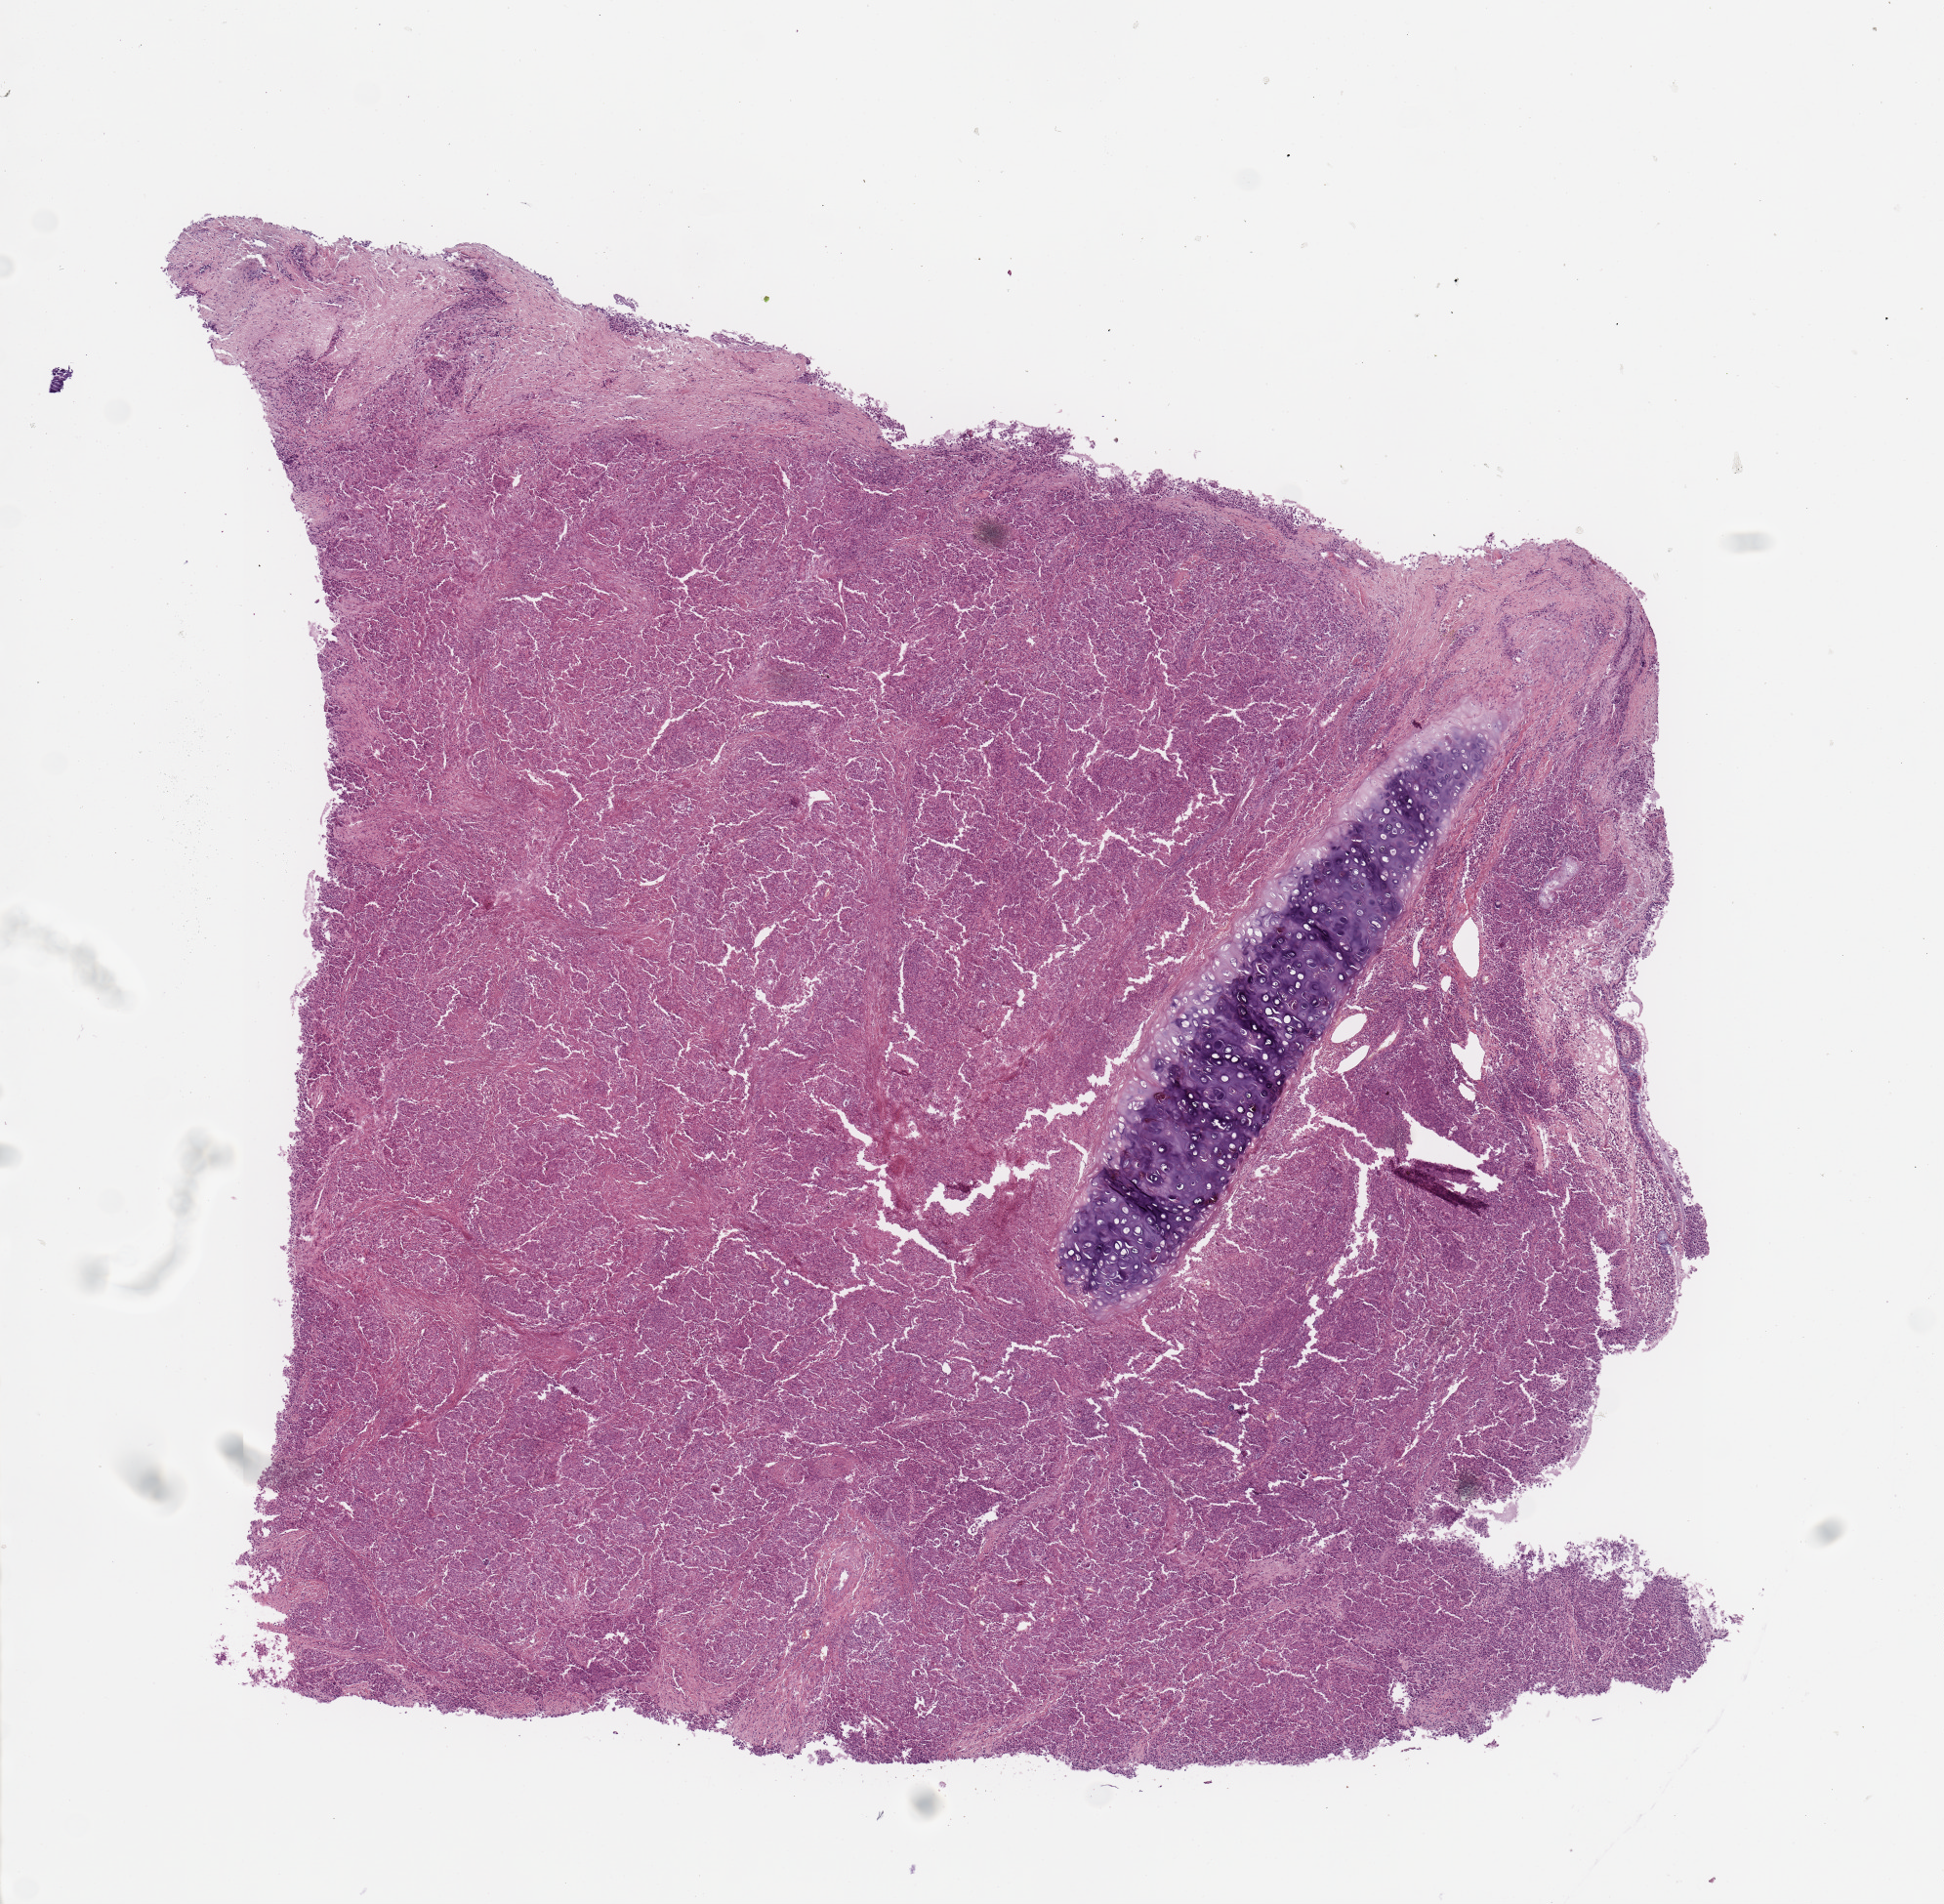
H&E-stained whole-slide image, whole scanned area (about 7.9 x 7.7 mm, slide scanned at 20x) shown as a low-resolution overview; tumour tissue sample, sampled site: lung. Patient: male, age 65 years. Histologic grade: GX (grade cannot be assessed). Slide review estimates, as recorded: tumour nuclei 85%, necrosis 0%.
Histologic diagnosis: Squamous cell carcinoma, NOS. AJCC pathologic stage: IA. Primary tumour site (as recorded): left upper lobe.